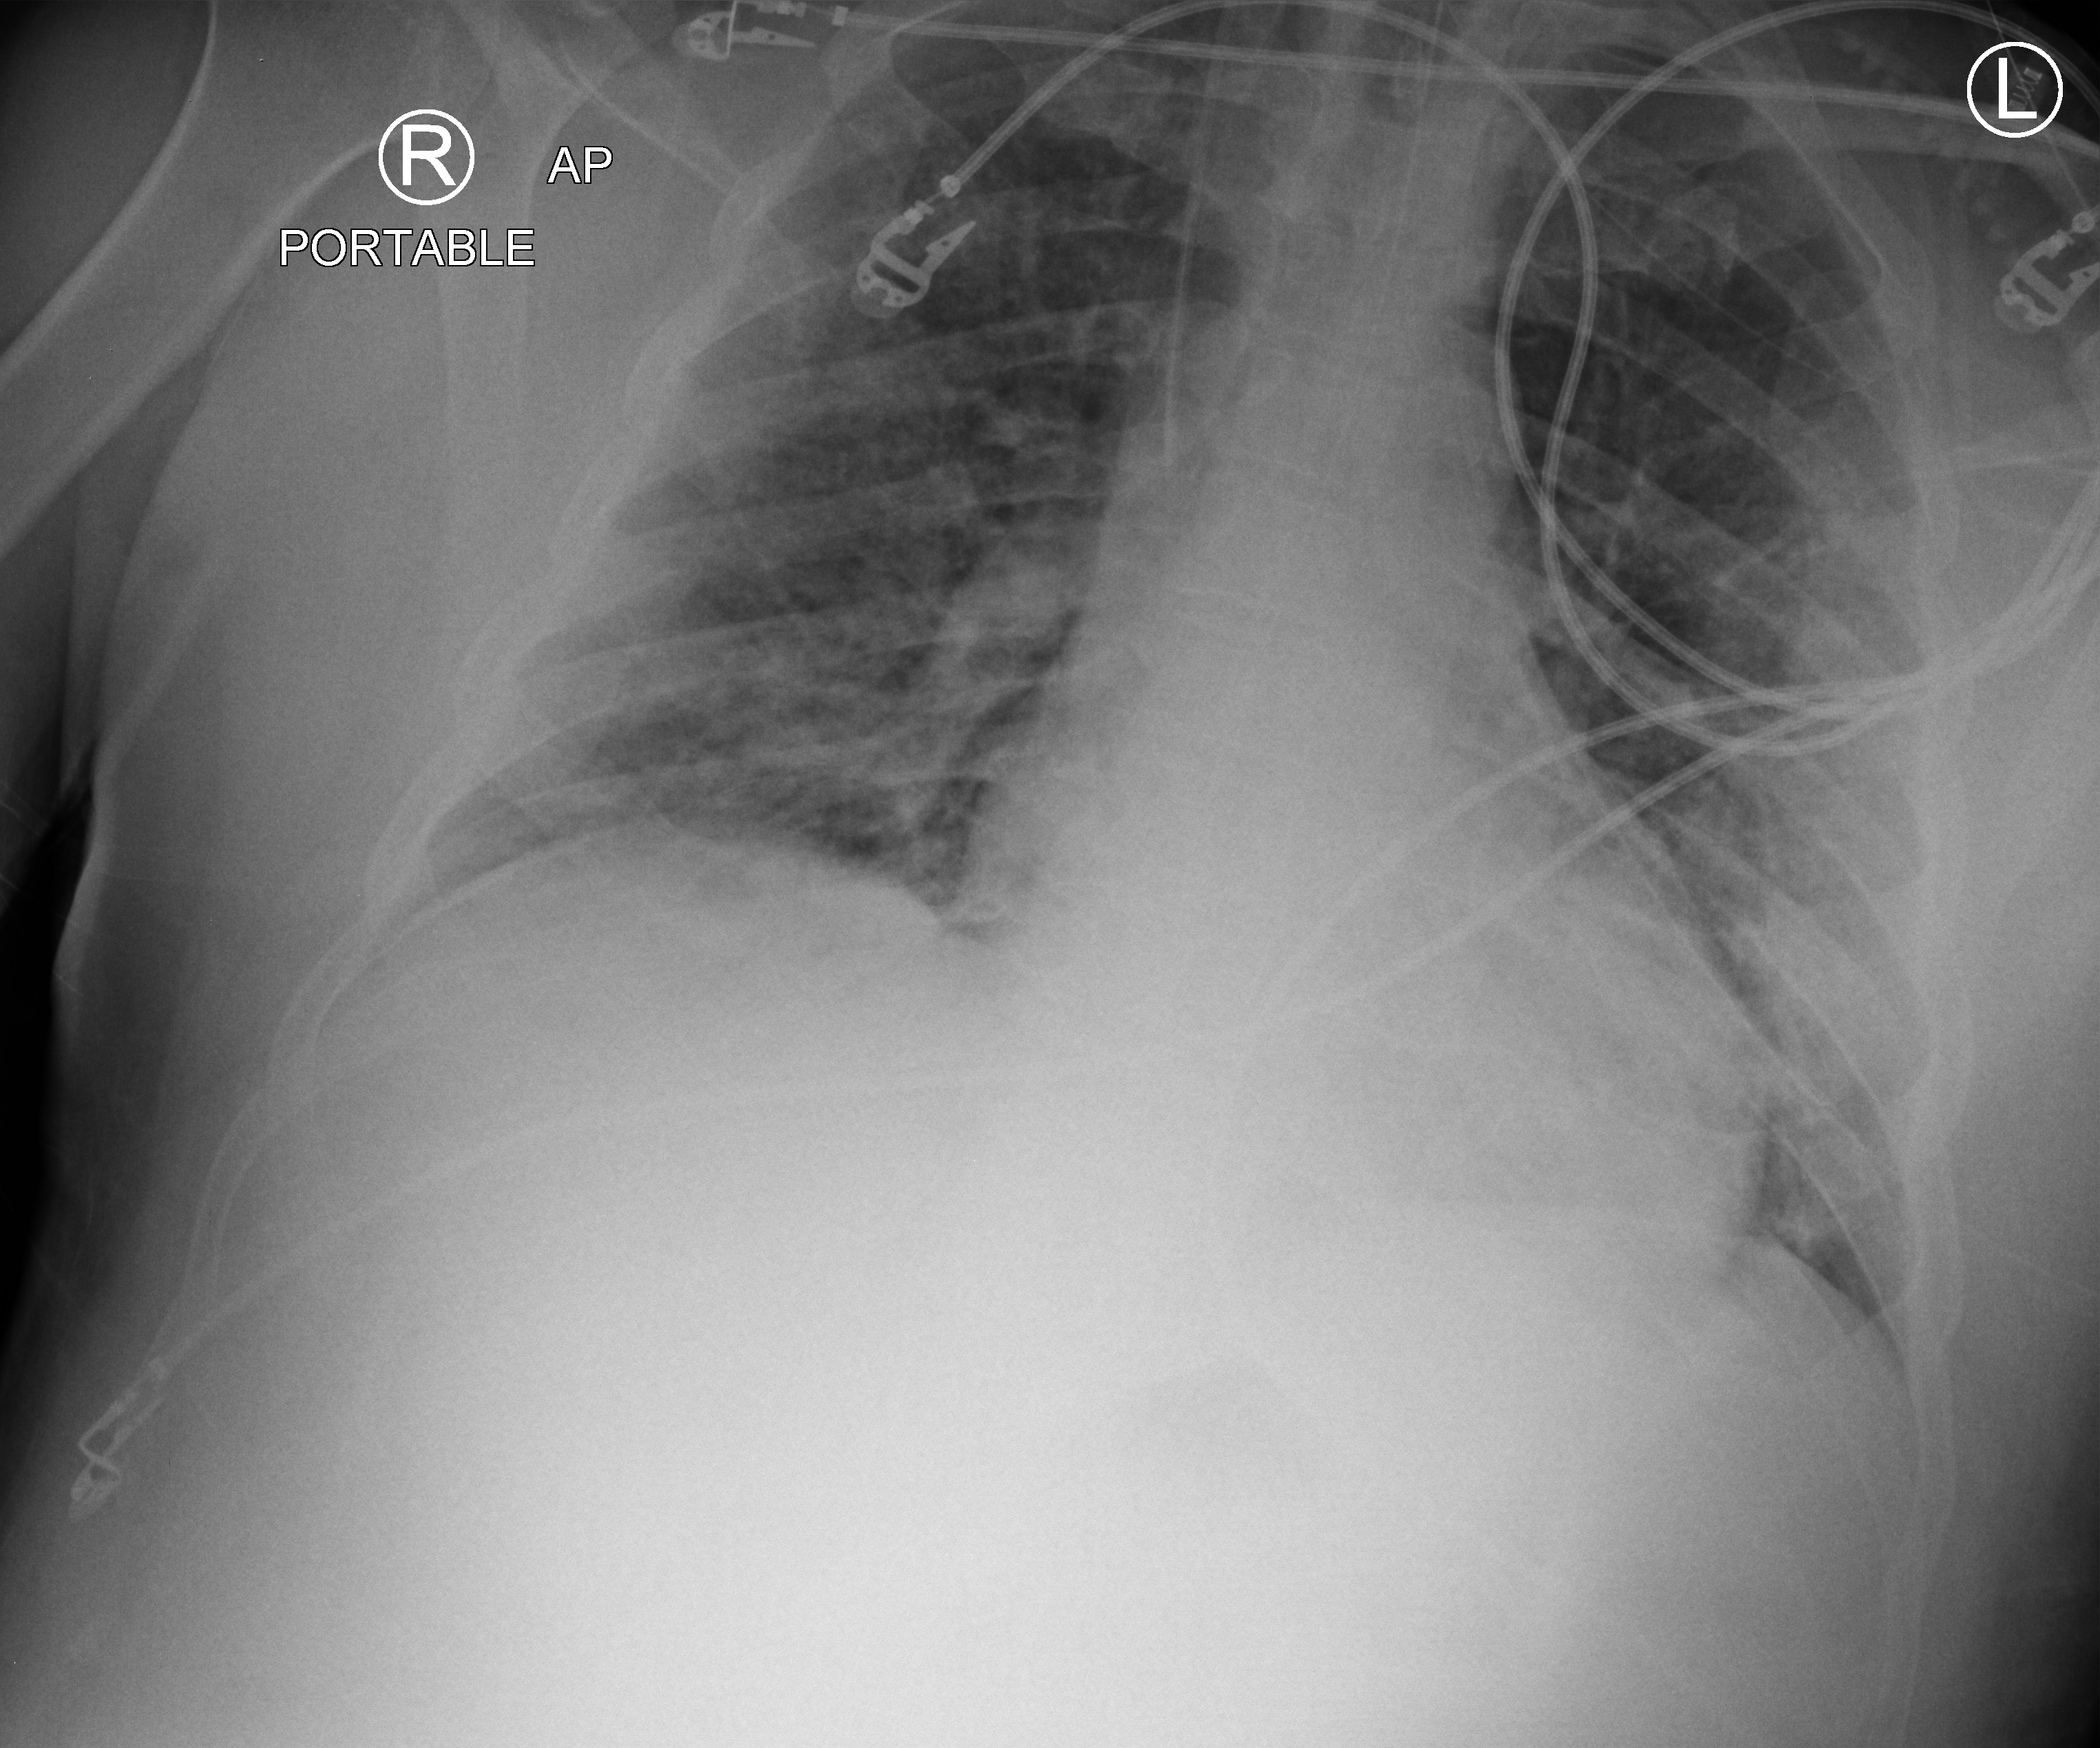
Bedside chest radiograph (computed radiography); anteroposterior (AP) projection. Patient hospitalised with COVID-19; male, aged 18–59 years.
Admission-level facts for this patient (not findings on this image; timing relative to this image not recorded): mechanically ventilated during this hospital stay: yes.